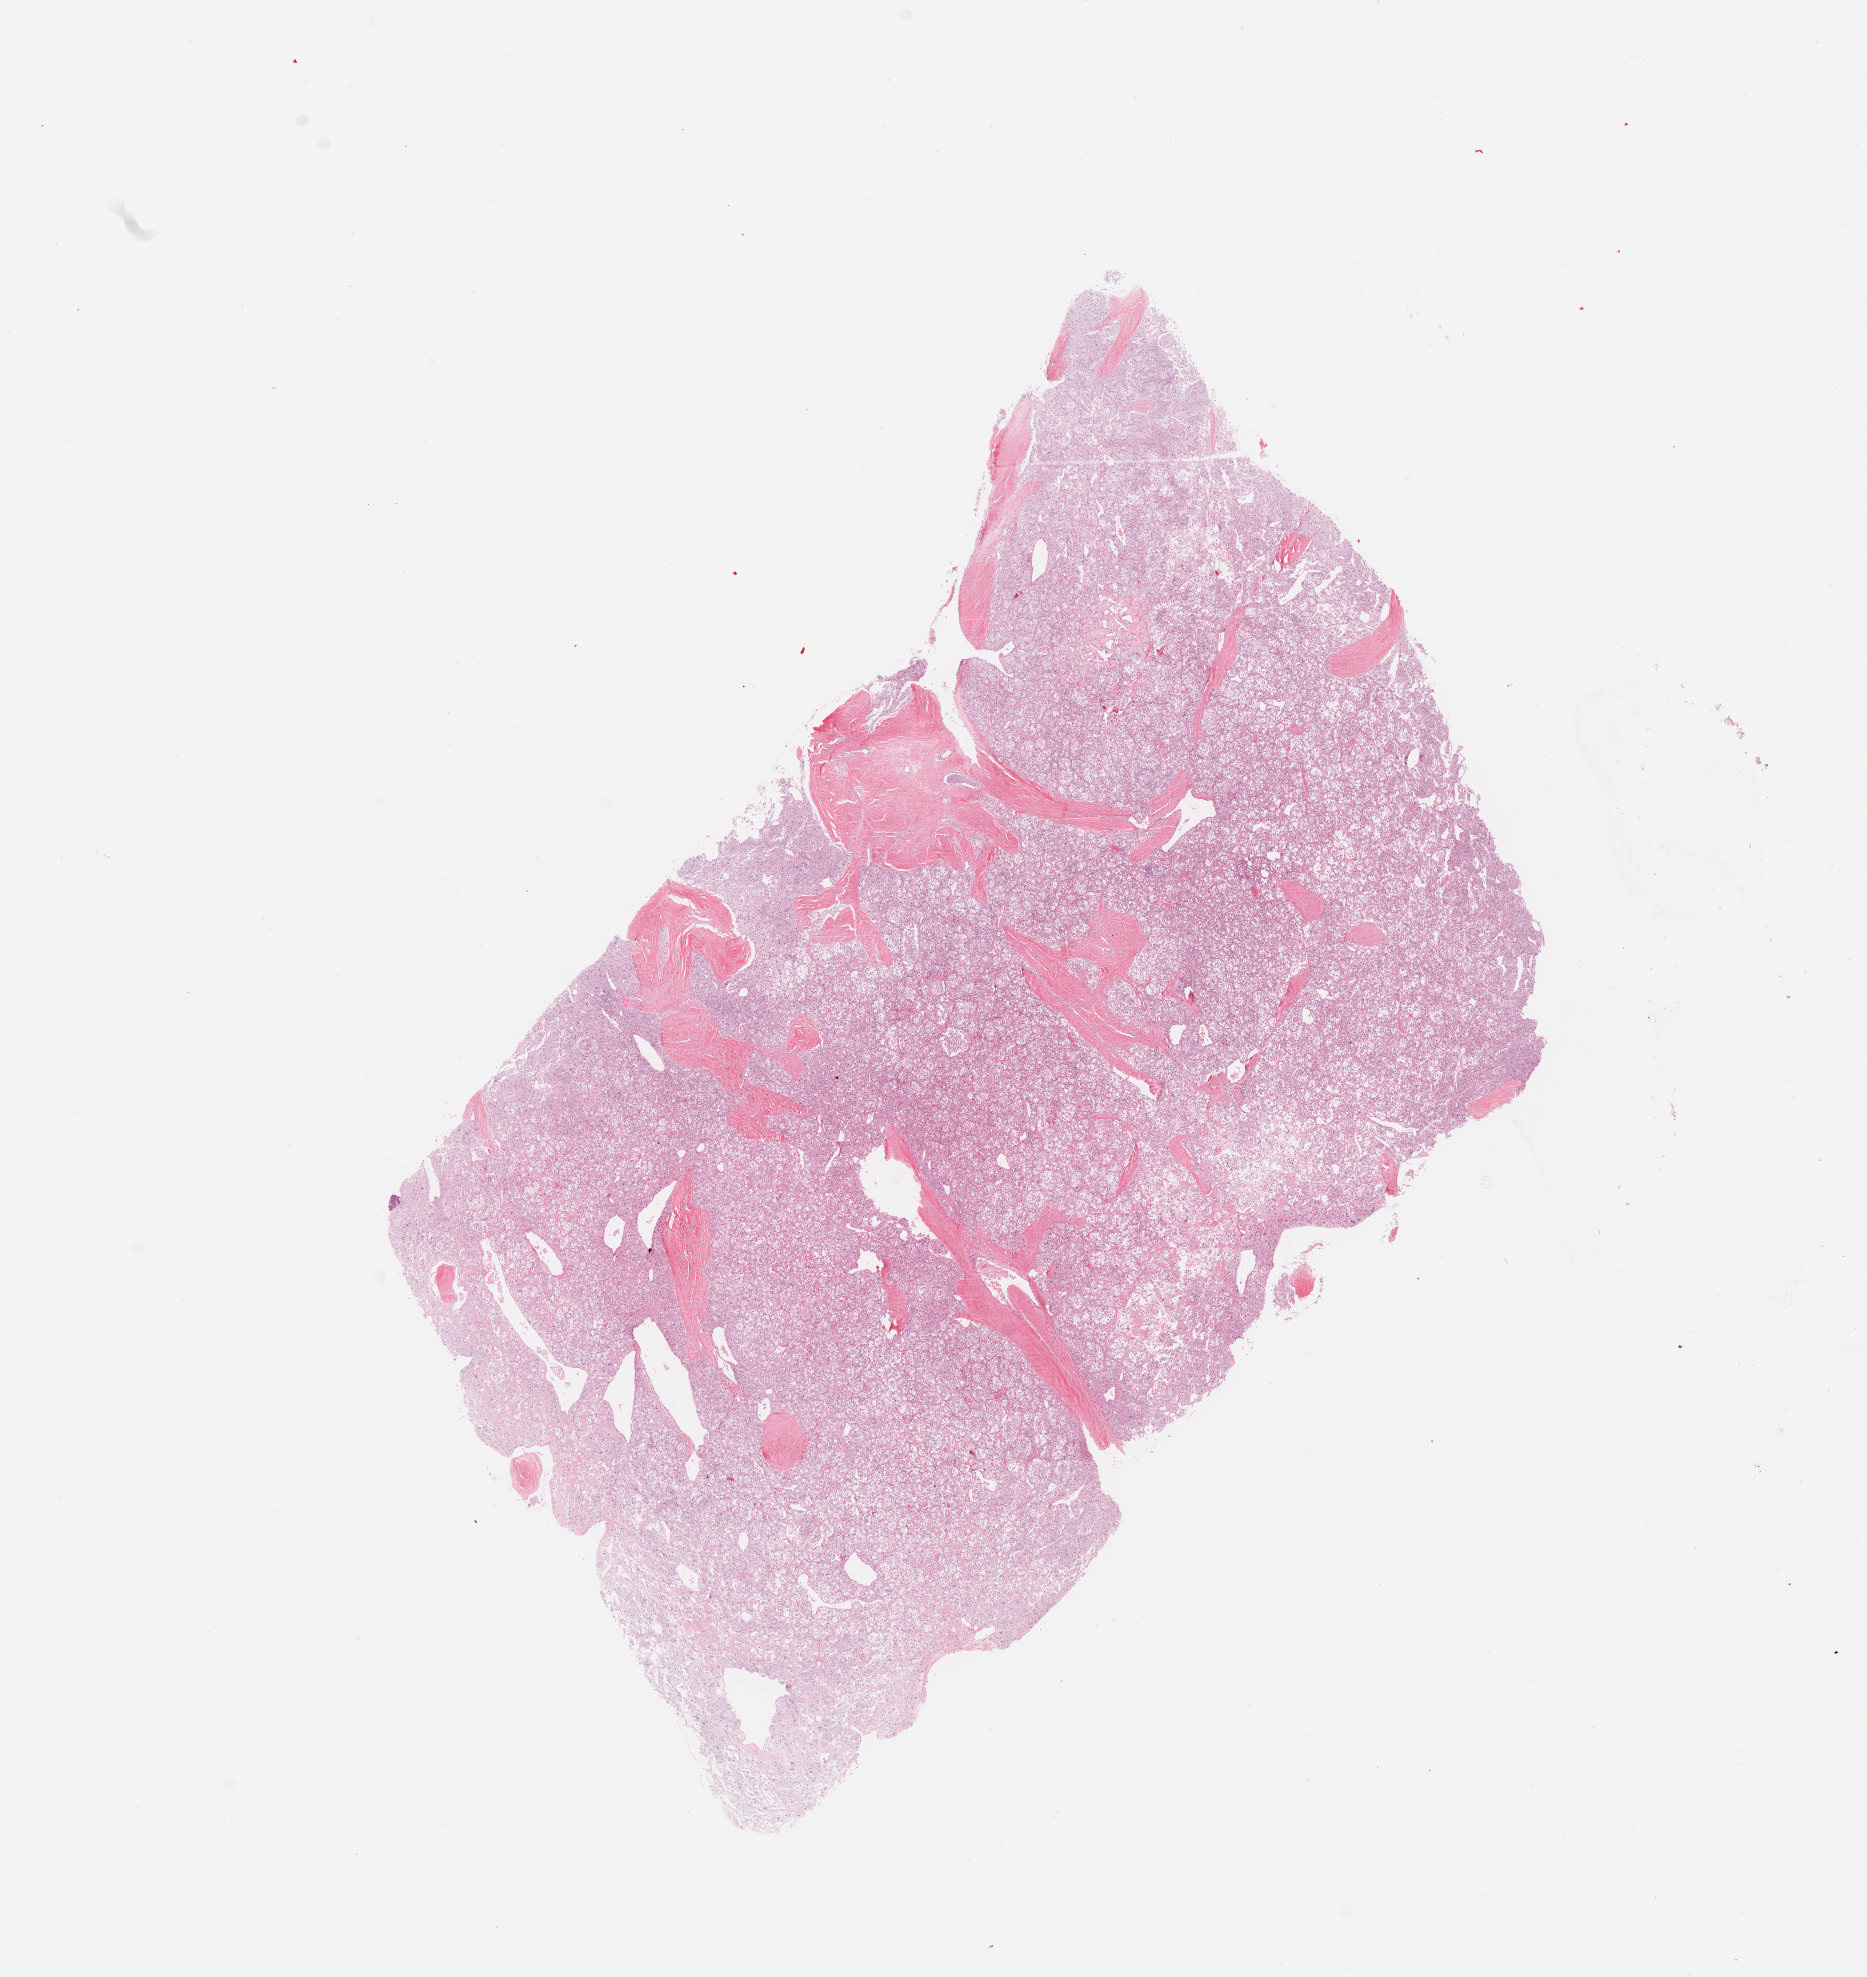
Digitized Hematoxylin and eosin (H&E) stained tissue section (whole slide), a low-resolution overview of the entire scanned area, about 14.8 x 15.6 mm. Patient: male, age 50 years.
Patient diagnosis (cohort enrolment): sarcoma (site not recorded at cohort level).